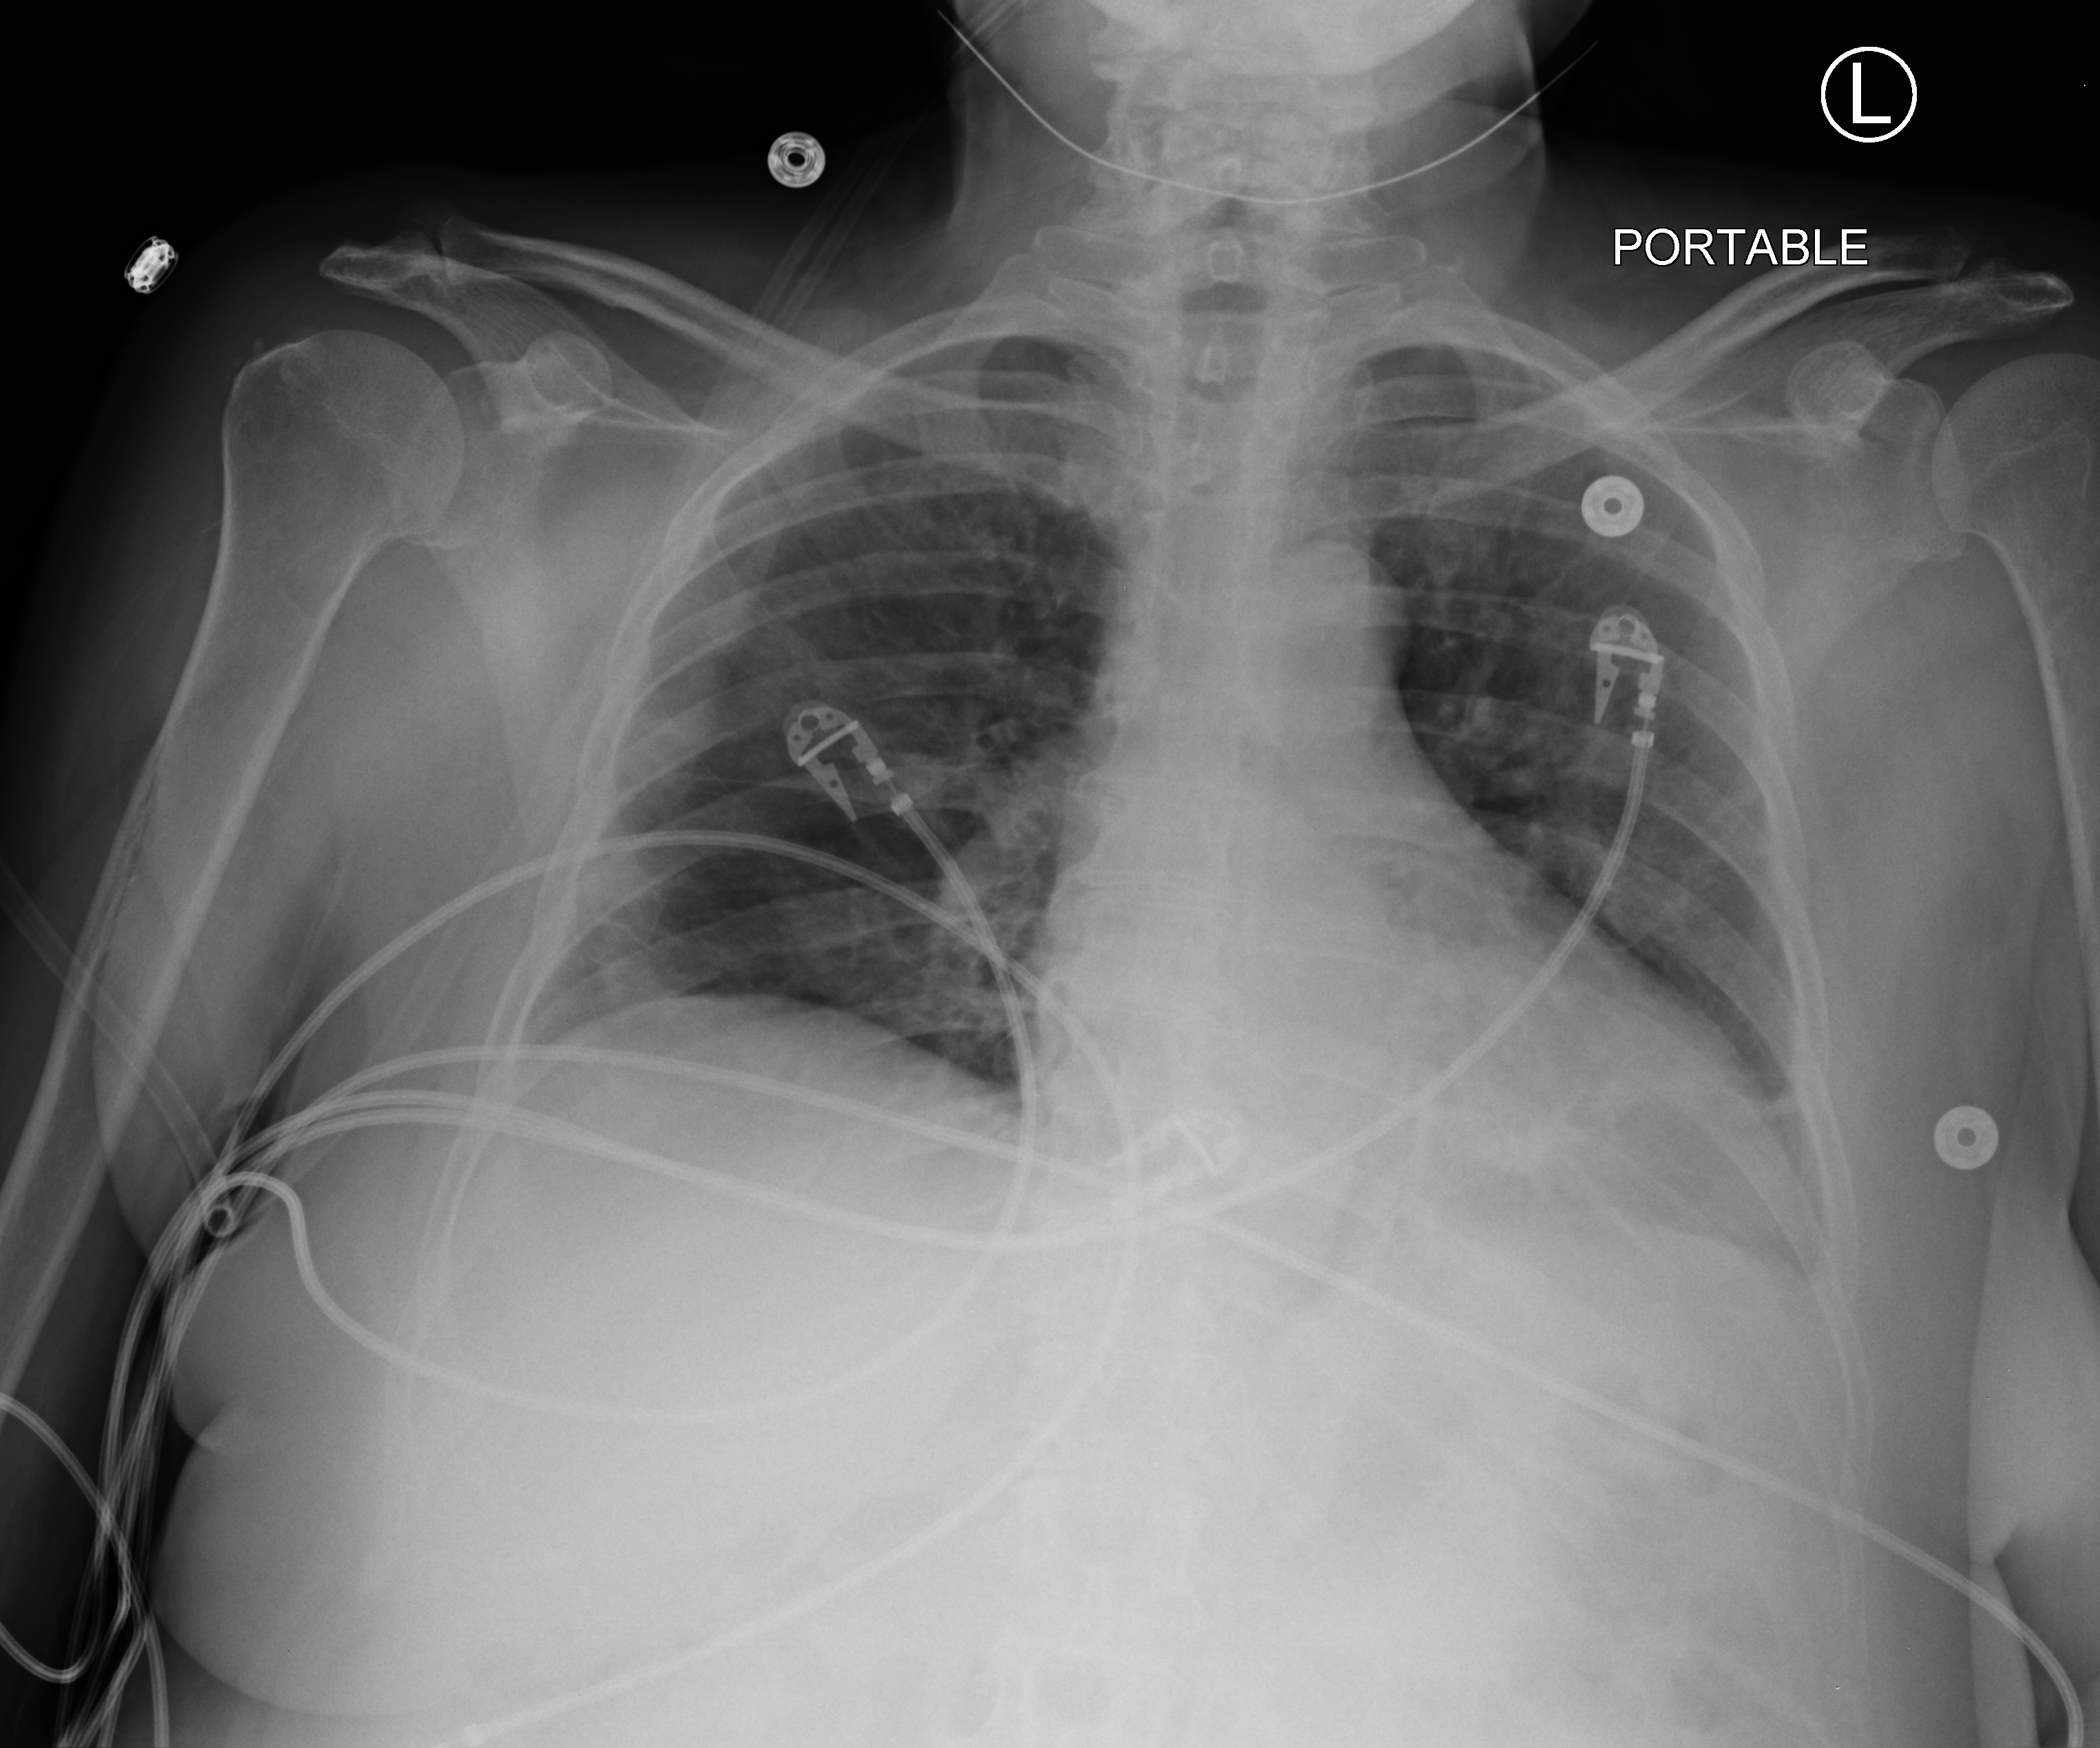
Portable chest radiograph. Female patient hospitalised with COVID-19, age 60–74 years.
Hospital-stay facts (about this admission, not read from this image; timing relative to this image not recorded):
- admitted to intensive care during this hospital stay: no
- mechanically ventilated during this hospital stay: no